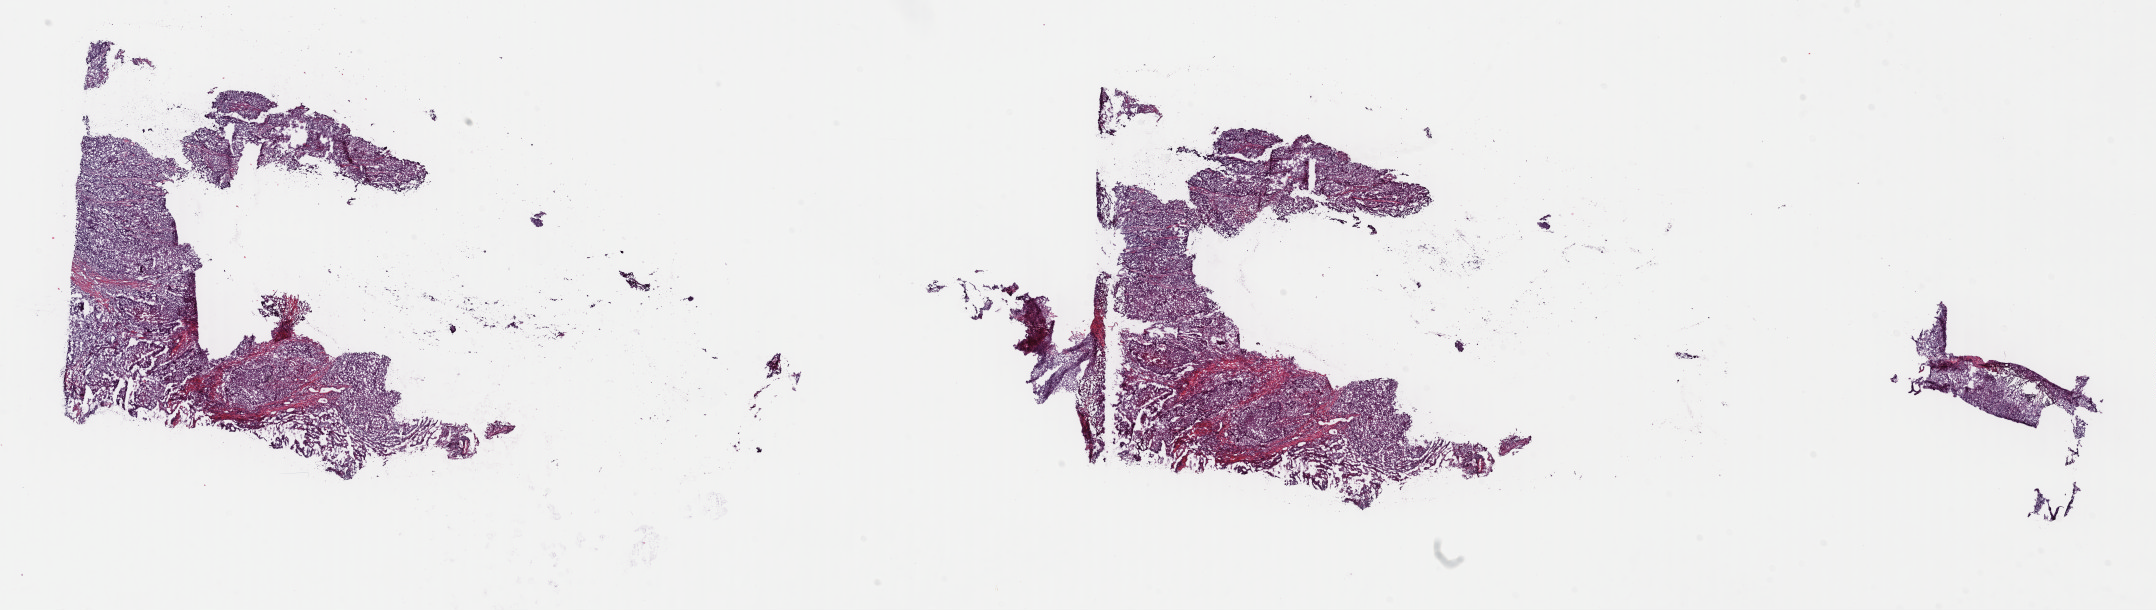
Whole-slide histology image, Hematoxylin and eosin (H&E) stained, low-resolution overview of the scanned area, about 33.9 x 9.6 mm. Frozen section from the top of the tissue portion. Lung, primary tumour sample. Male, age 65 years at initial diagnosis. Composition of this section per pathologist review: tumour cells 50%, tumour nuclei 65%, normal cells 0%, stromal cells 30%, necrosis 20%. Inflammatory infiltration, as recorded: lymphocyte infiltration 15%, monocyte infiltration 3%, neutrophil infiltration 3%.
Diagnosis: Squamous cell carcinoma, NOS (lower lobe, lung). AJCC pathologic stage: IA (7th edition). Laterality: right.